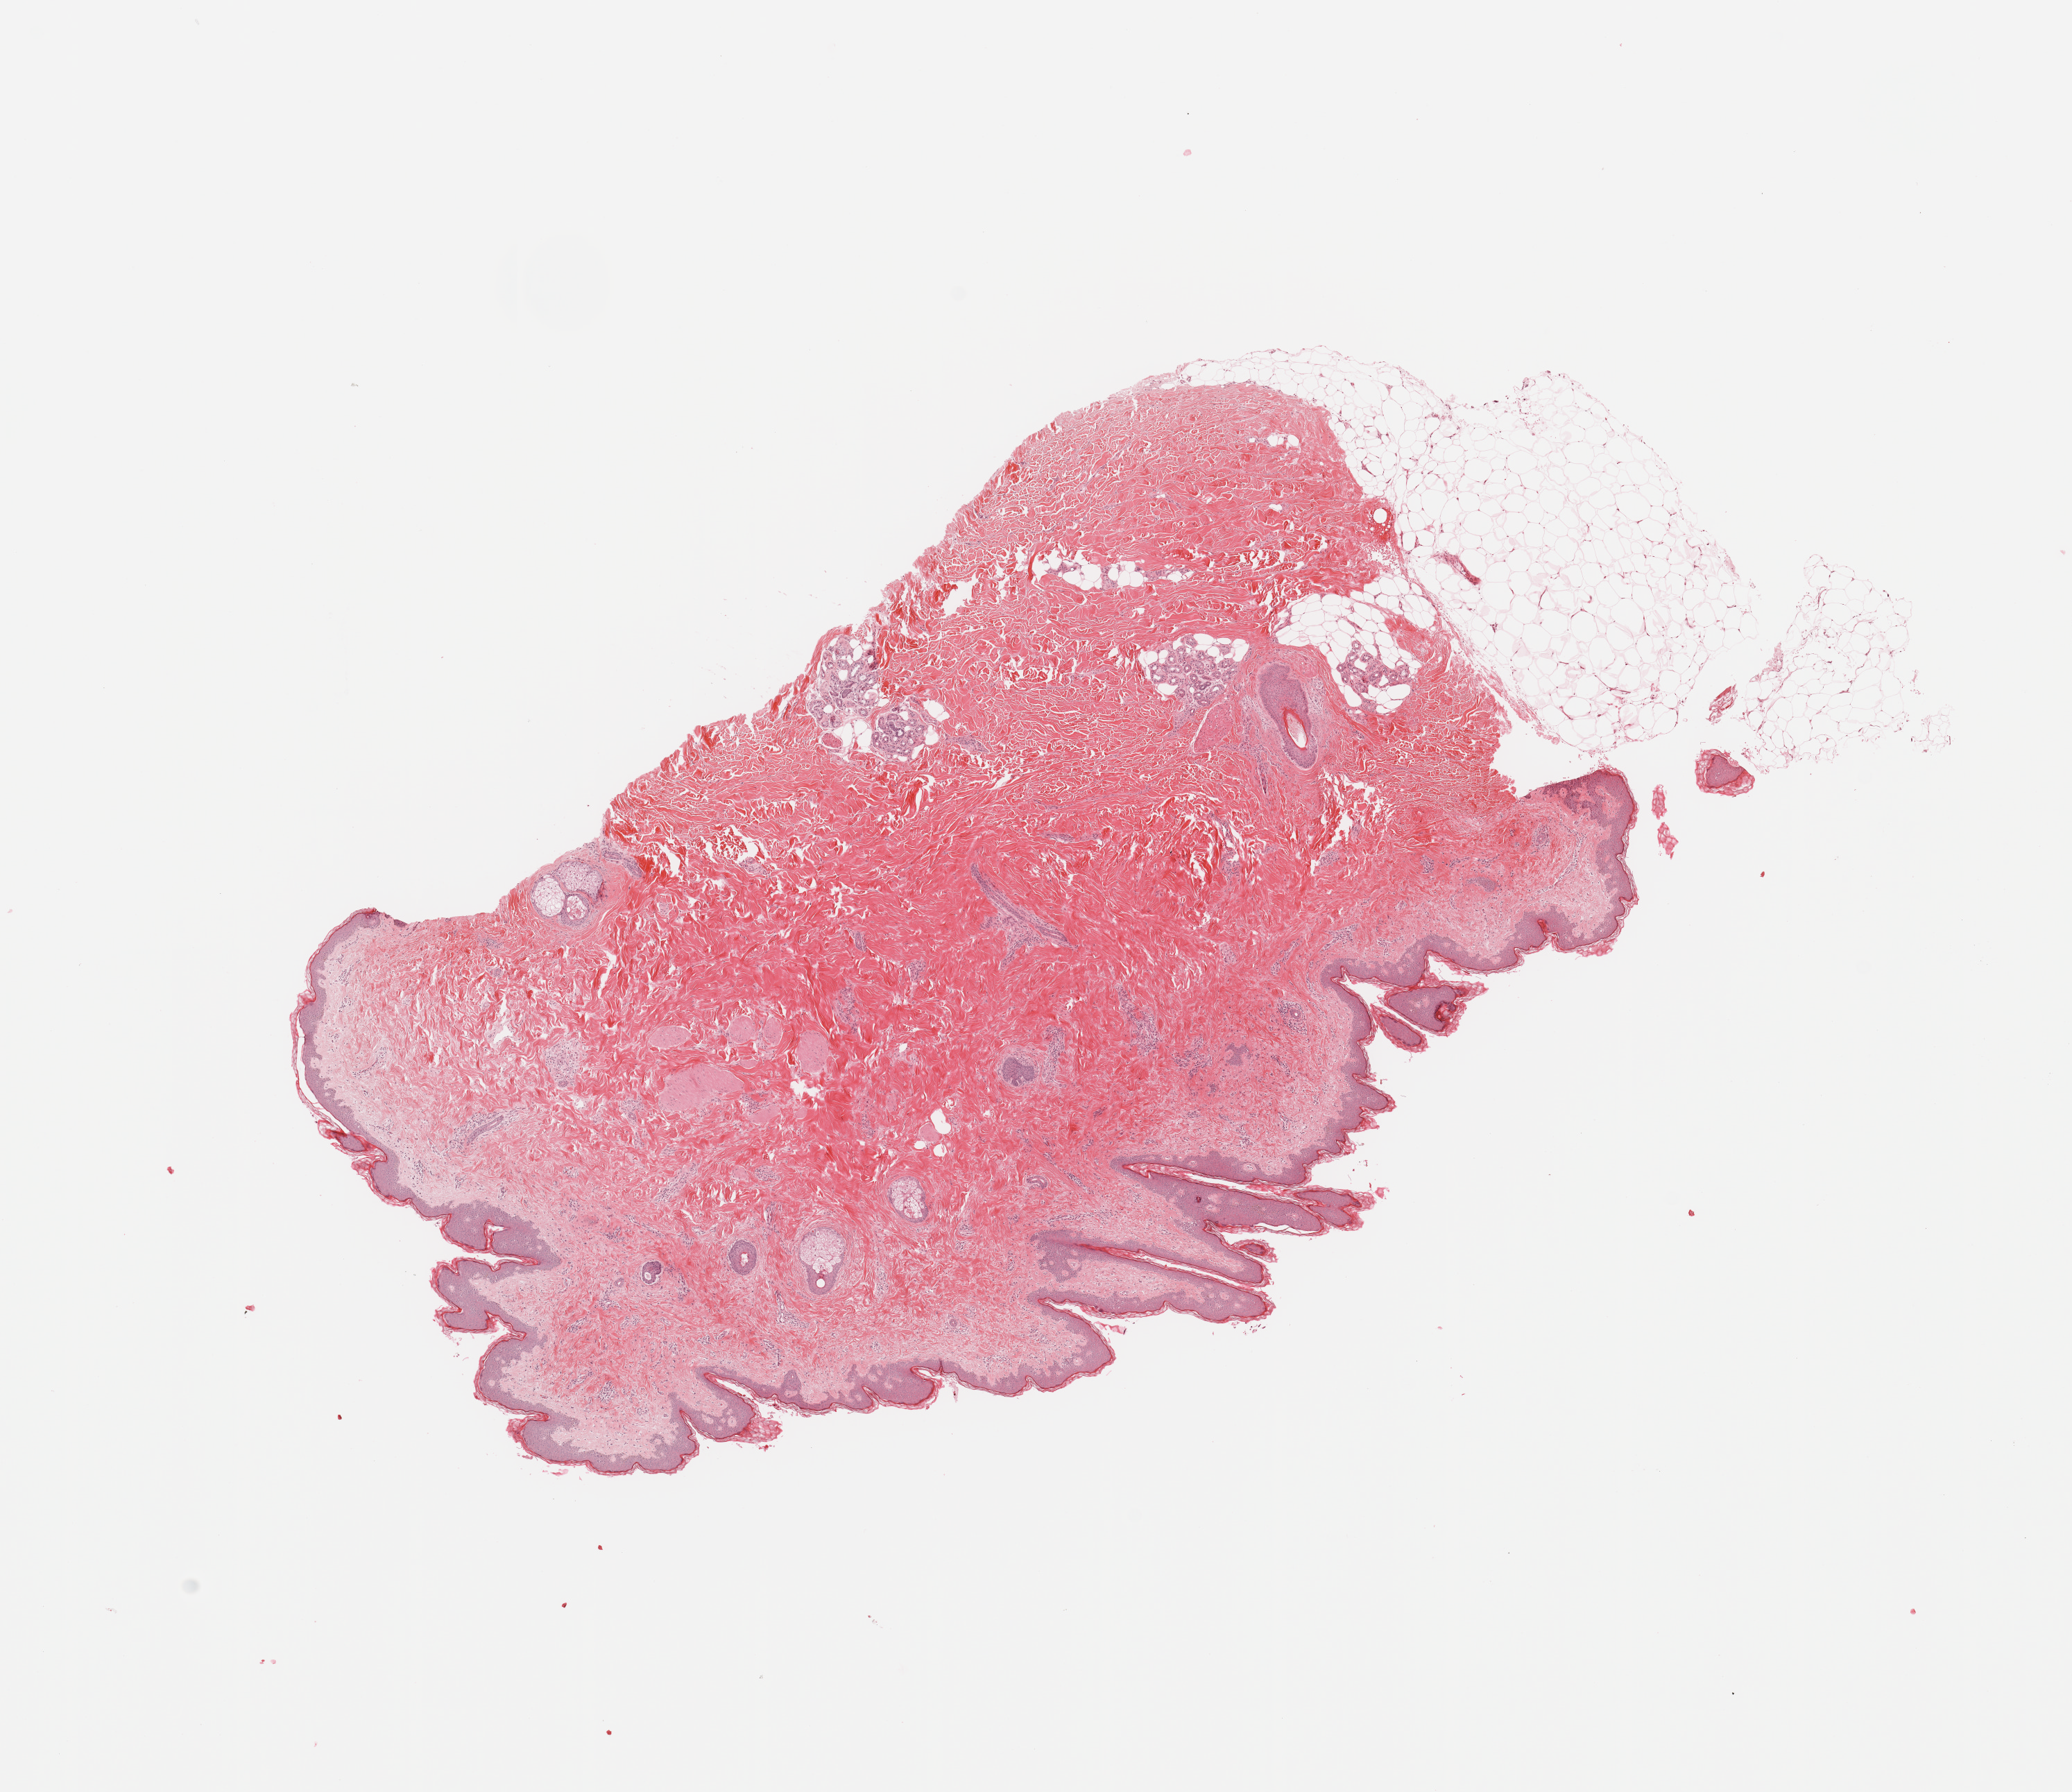
Whole-slide histology image, H&E — whole scanned area (about 11.8 x 10.2 mm, acquisition: 20x scan) shown as a low-resolution overview, normal (non-tumour) tissue sample. Patient: male, age 75 years.
• this section: normal (non-tumour) tissue from the same patient
• patient diagnosis (cohort enrolment): sarcoma (site not recorded at cohort level)